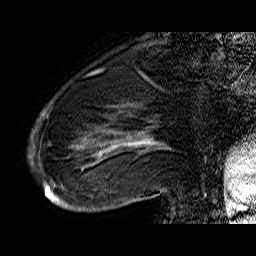
Breast MRI (dynamic contrast-enhanced), one sagittal slice. Slice 15 of 60 in the series (ordered by position). Dynamic contrast-enhanced series, time point 2 of 6 at this slice position (early post-contrast). 1.5 T. TE 6.4 ms, TR 32.9 ms. 4 mm slice thickness. 256 × 256 image matrix. Female patient. Case-level facts recorded for this patient, not image findings: setting: breast cancer imaged before/during neoadjuvant chemotherapy; receptor status: HR-positive, HER2-negative.
Structures marked on this image (semi-automatic segmentation, software-assisted and operator-edited):
- analysis volume of interest (the breast-tissue region the enhancement analysis was run in; not a lesion): bounding box (x1, y1, x2, y2) in pixels: (44, 74, 176, 210)
- tumour enhancement mask (voxels above the 100 % enhancement threshold inside the analysis volume of interest): (44, 132, 161, 207)